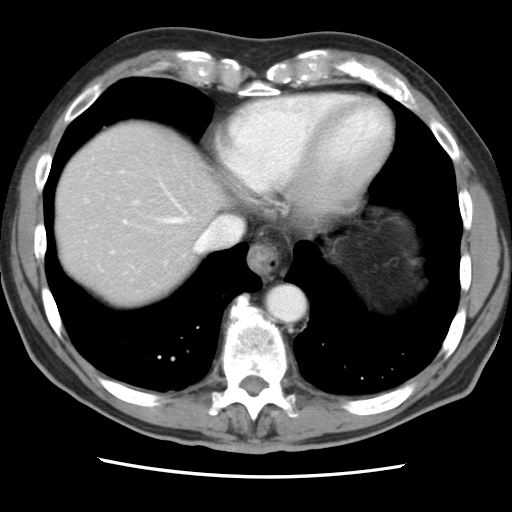
Contrast-enhanced abdominal CT, one axial slice. Slice 75 of 83 in the series (ordered by position). Intravenous contrast given. Soft-tissue window (W 400 / L 40 HU). 5 mm slice thickness. 512 × 512 image matrix, field of view 321 × 321 mm. Male patient, age 69 years. Case-level facts recorded for this patient, not image findings: diagnosis: colorectal cancer liver metastases, imaged before liver resection; multiple liver metastases: yes; largest metastasis: 3.5 cm; disease in both lobes: no.
Annotated regions visible in this slice (outlined manually by an expert reader):
- hepatic veins: box from (x=158, y=211) to (x=242, y=252) px
- liver: (x=57, y=121)–(x=222, y=307)
- planned liver remnant (the part of the liver to remain after resection): (x=57, y=154)–(x=213, y=307)
- portal vein (with intrahepatic branches): (x=123, y=219)–(x=127, y=224)